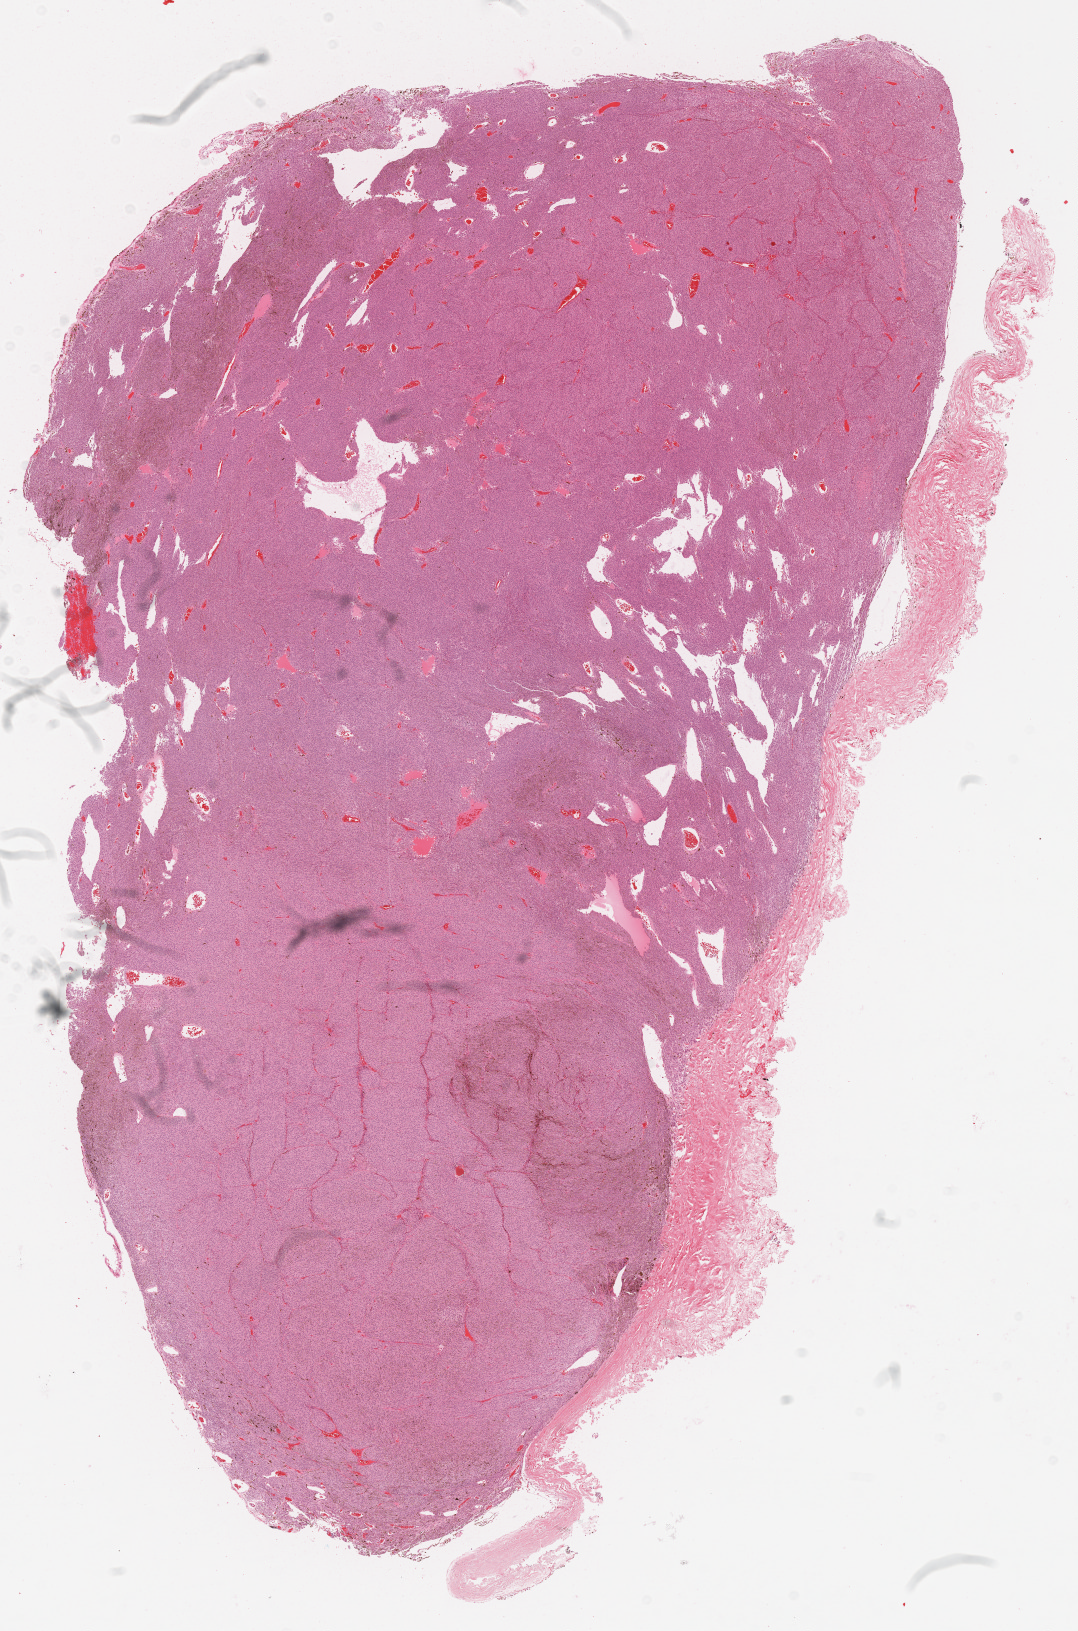
Whole-slide histology image, H&E — shown as a low-resolution overview of the whole scanned area (about 8.7 x 13.2 mm). FFPE section. Uvea, primary tumour sample. Patient: male, age at initial diagnosis 22 years.
Histologic diagnosis: Mixed epithelioid and spindle cell melanoma (choroid).